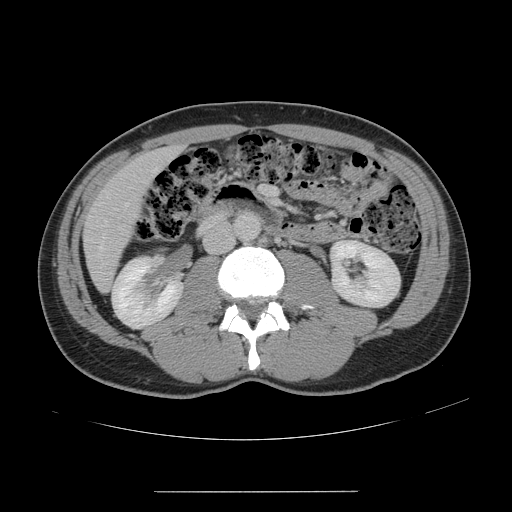
Contrast-enhanced abdominal CT, one axial slice. Slice 47 of 178 in the series (ordered by position). 120 kVp. Soft-tissue window (W 400 / L 40 HU). 512 × 512 image matrix, field of view 401 × 401 mm. Male patient, age 53 years. Case-level facts recorded for this patient, not image findings: diagnosis: colorectal cancer liver metastases, imaged before liver resection; multiple liver metastases: yes; largest metastasis: 2.4 cm; disease in both lobes: no.
Annotated regions visible in this slice (outlined manually by an expert reader):
- hepatic veins: bounding box [x1, y1, x2, y2] px = [98, 168, 158, 257]
- liver: [85, 148, 177, 291]
- portal vein (with intrahepatic branches): [265, 189, 267, 193]